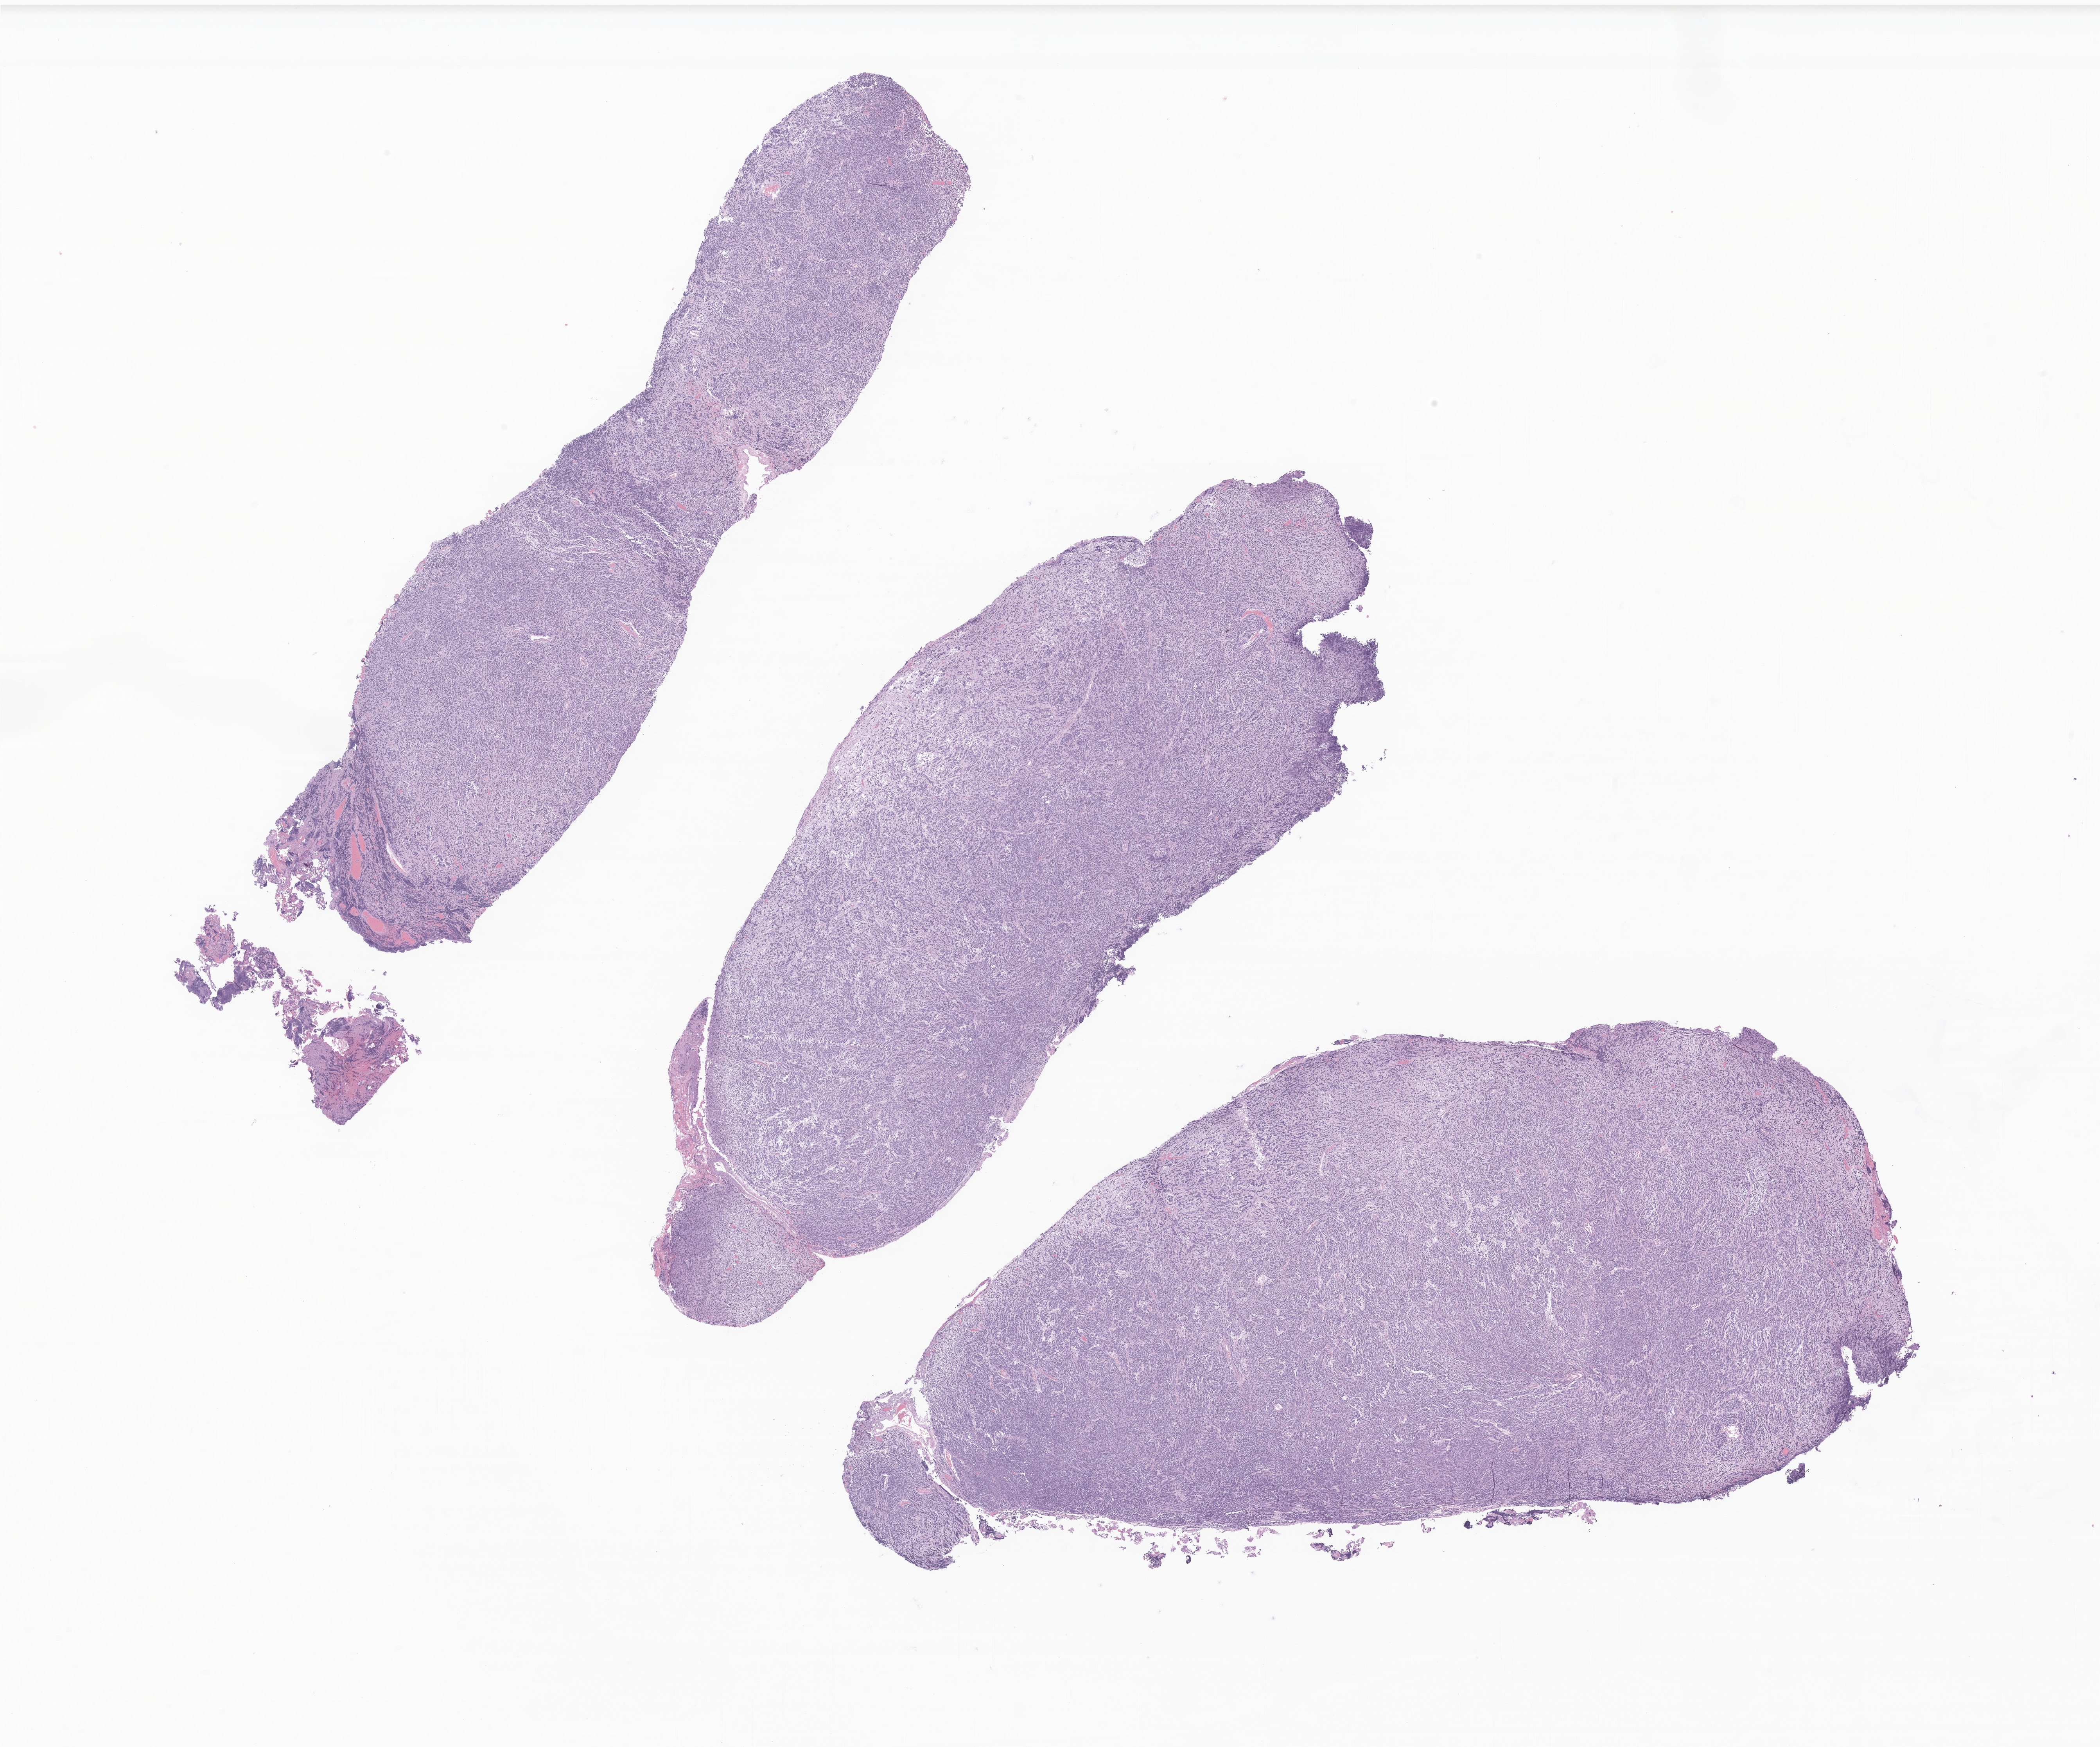
Haematoxylin and eosin whole-slide image of tumor tissue from the brain — a low-resolution overview of the entire scanned area, about 22.6 x 18.8 mm; formalin-fixed, paraffin-embedded (FFPE) tissue. Patient male; age 47 months.
Recorded diagnosis: Medulloblastoma, NOS.